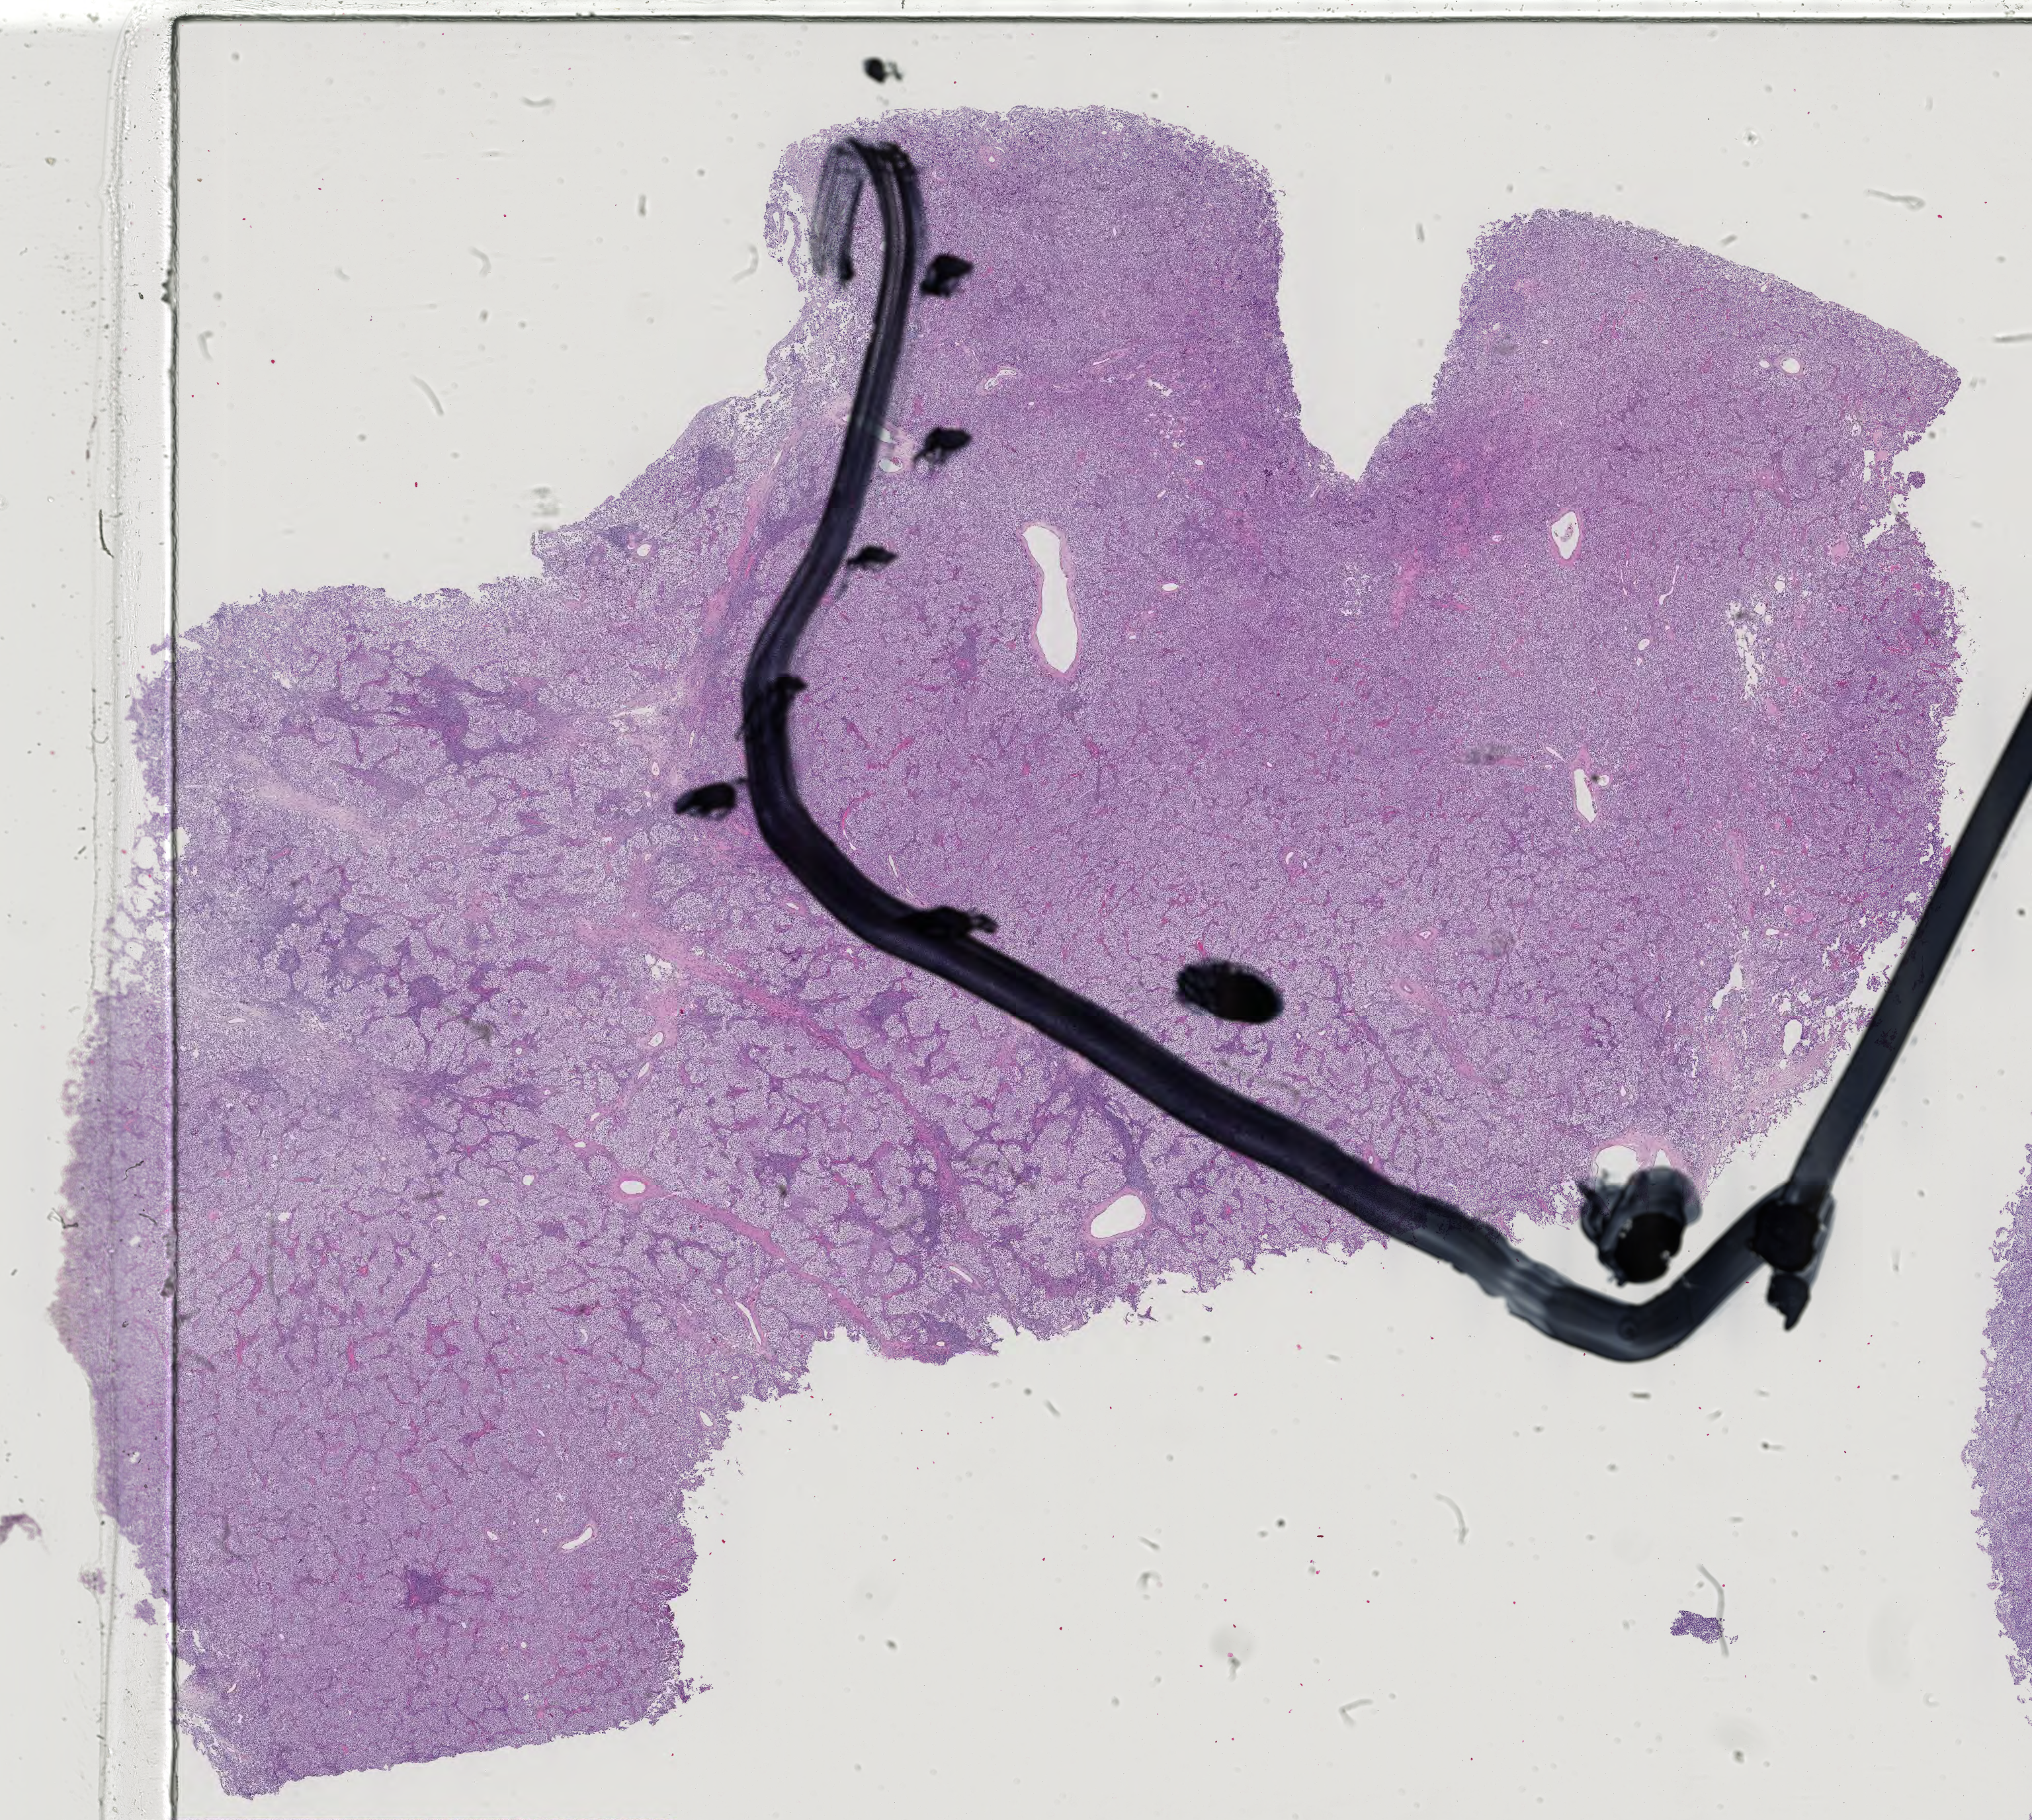
Whole-slide histology image, H&E, a low-resolution overview of the entire scanned area, about 22.4 x 20.1 mm (from a 40x scan); formalin-fixed paraffin-embedded (FFPE) diagnostic section; primary tumour sample from the testis. Patient: male, age at initial diagnosis 28 years.
Laterality: right. AJCC pathologic stage: IS (7th edition). TNM: T1 N0 M0. Diagnosis: Seminoma, NOS.